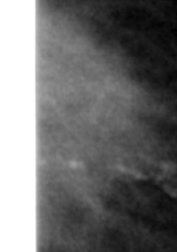
Crop from a digitized film mammogram around one marked abnormality, right breast, MLO view.
Finding: mass, shape irregular, margins ill defined; BI-RADS assessment category 4; pathology (as recorded): malignant.